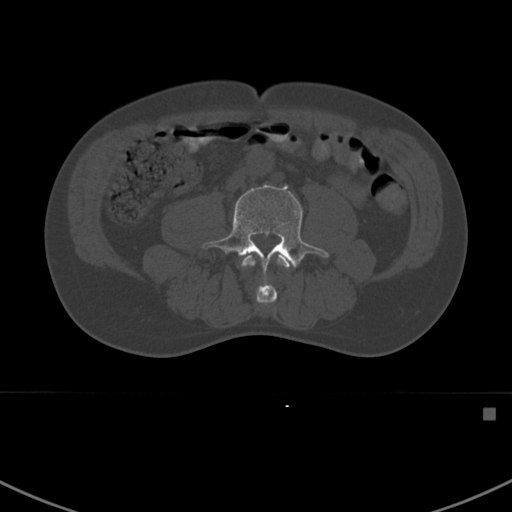
CT including the spine, one axial slice; slice 246 of 412 in the series (ordered by position); reconstruction kernel Br40s; bone window (W 1800 / L 400 HU); 1.5 mm slice thickness; 512 × 512 image matrix. Patient: male, 59 years. Case-level facts recorded for this patient, not image findings: primary cancer: prostate.
Outlined on this slice (semi-automatic segmentation, software-assisted and operator-edited):
- L3 vertebra: bounding box <241,254,294,305> (left, top, right, bottom; pixels)
- L4 vertebra: <202,184,328,285>